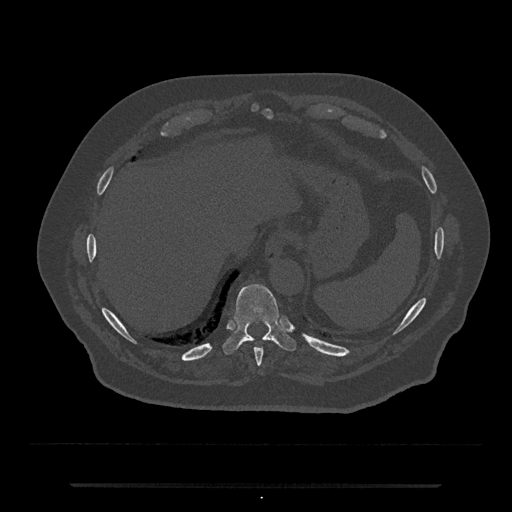
CT including the spine, one axial slice; position 721 of 797 along the scan axis; 120 kVp; bone window (W 1800 / L 400 HU); 512 × 512 image matrix, field of view 434 × 434 mm. Male patient, age 80 years. From the clinical record (not read from this slice): primary cancer: prostate; vertebrae with lytic lesions (as recorded): L1, T11.
Structures marked on this image (semi-automatically segmented with operator editing):
- T10 vertebra: bounding box [x1, y1, x2, y2] px = [222, 284, 296, 355]
- T9 vertebra: [254, 348, 263, 372]